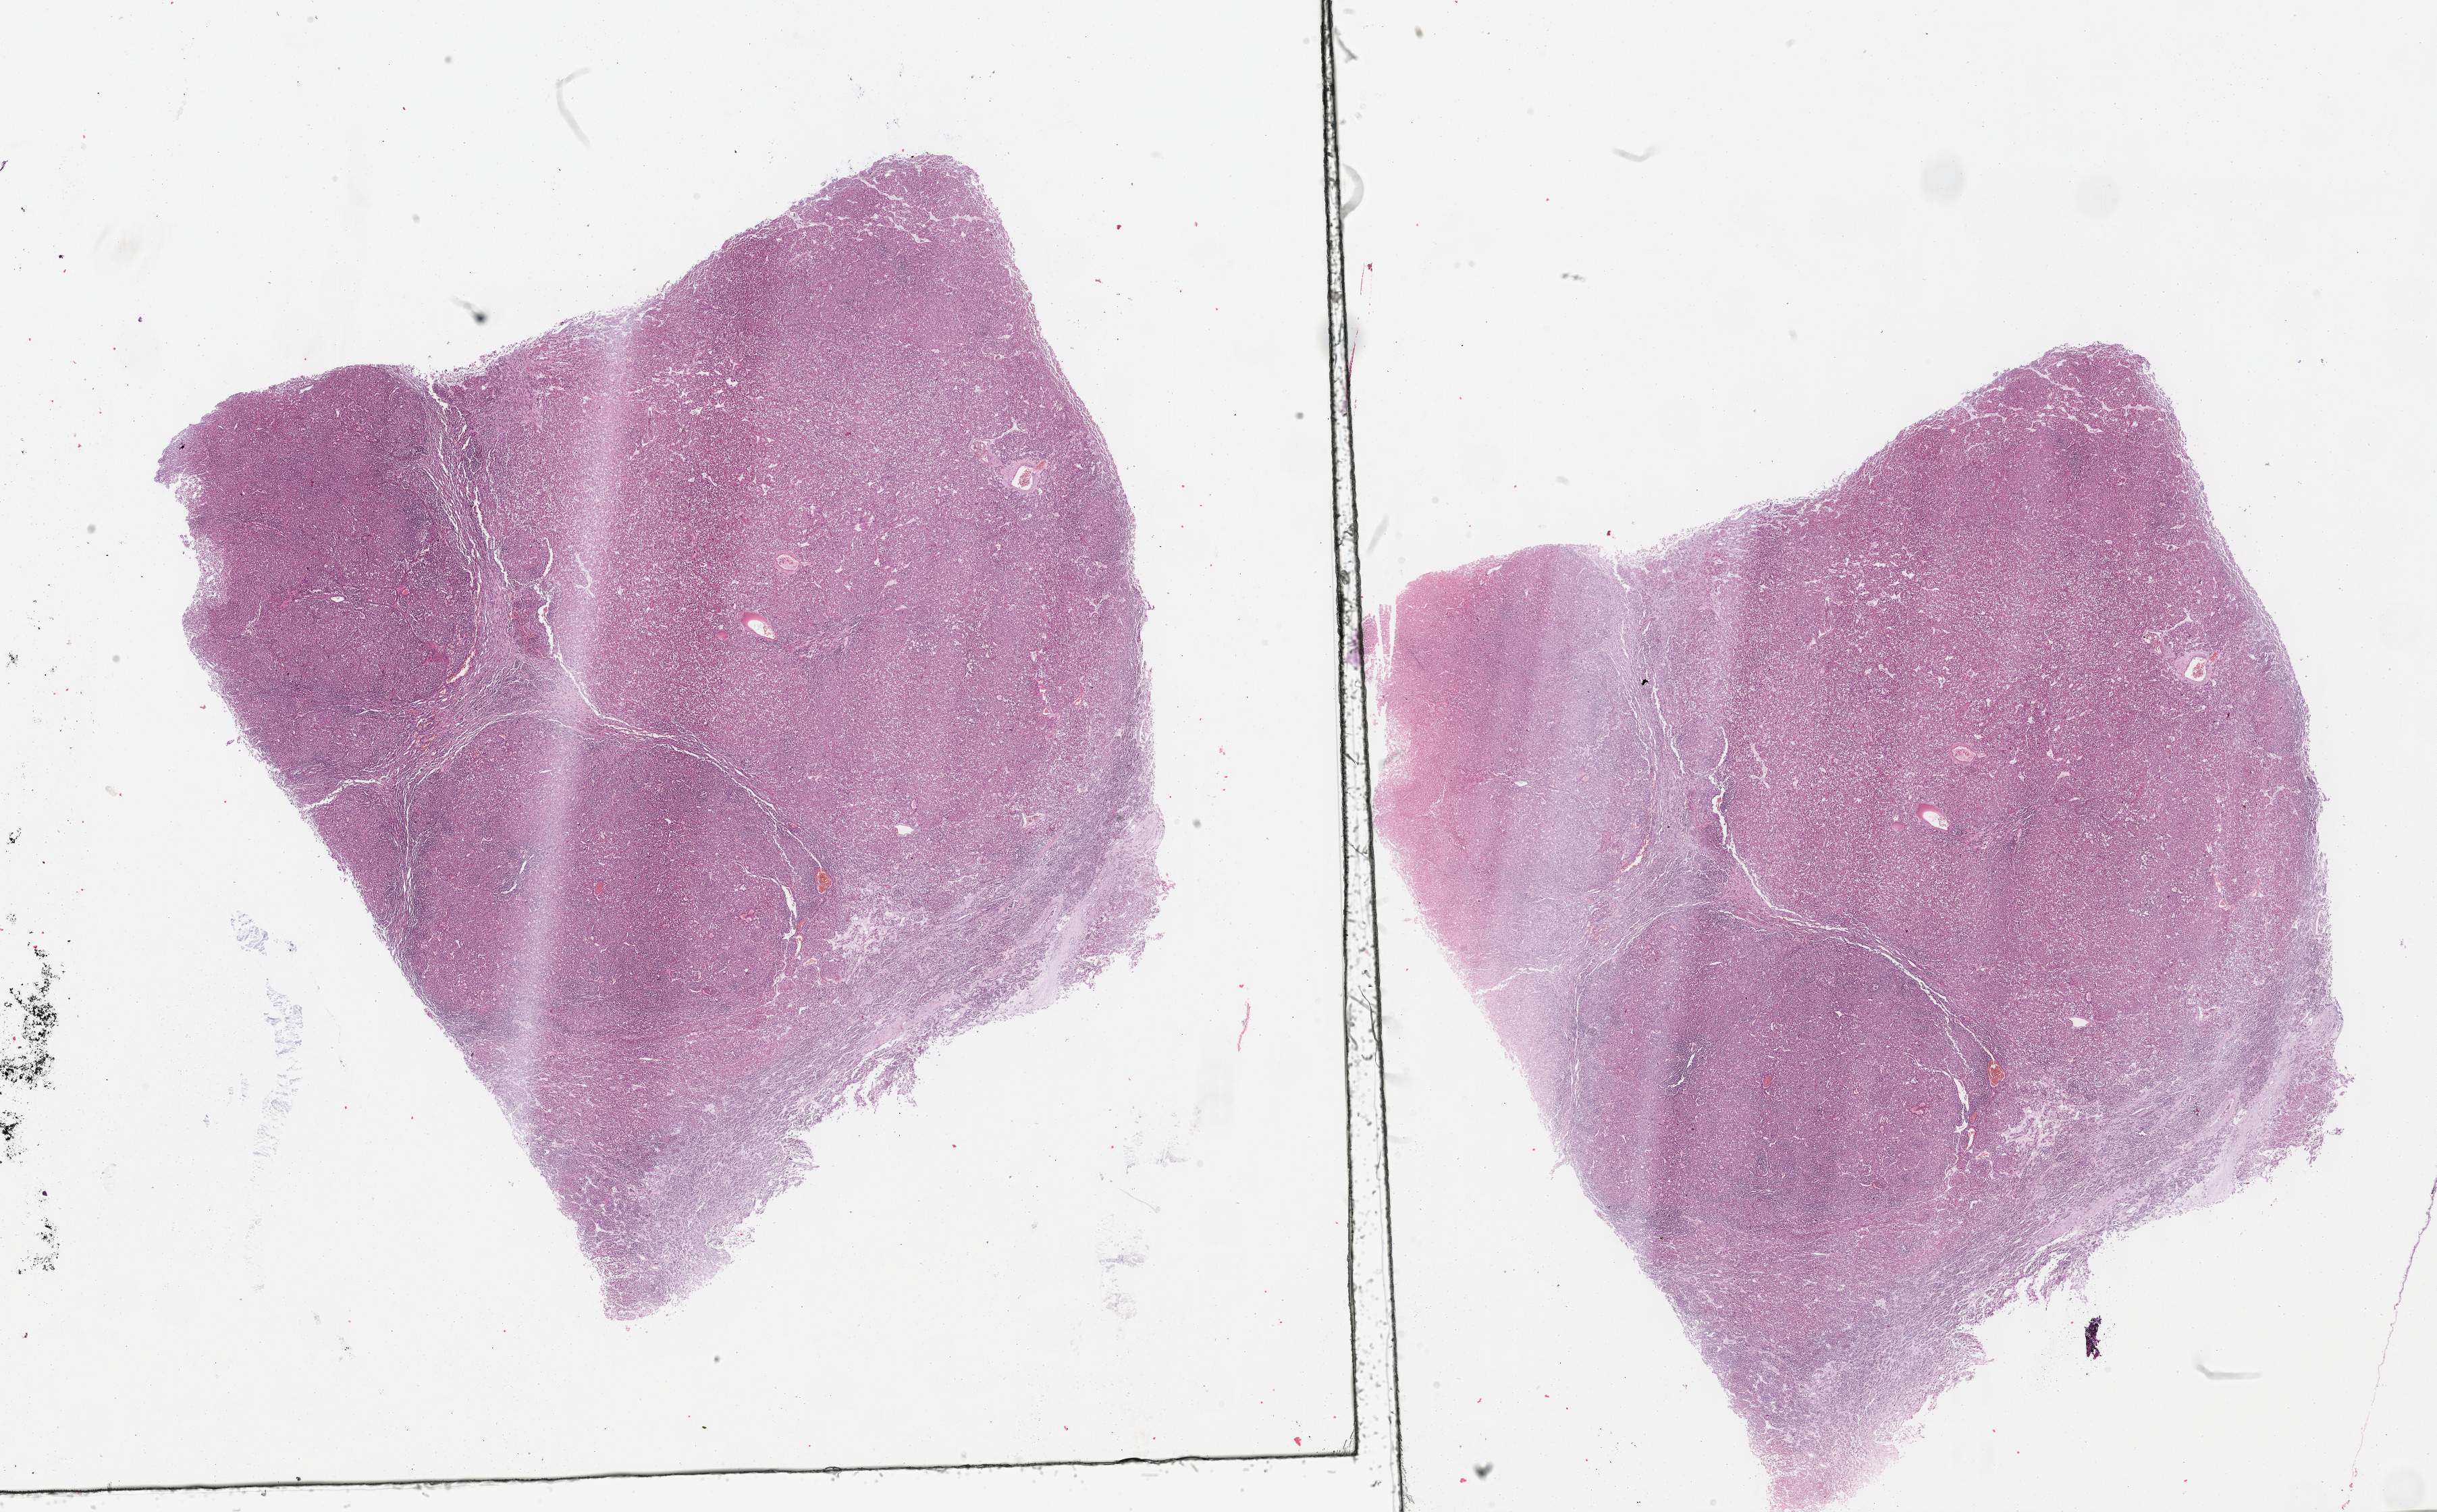
H&E-stained whole-slide image, low-resolution overview of the scanned area, about 29.2 x 18.1 mm (slide scanned at 40x), formalin-fixed paraffin-embedded (FFPE) diagnostic section, sample: primary tumour, bladder. Male, age 85 years at initial diagnosis. Histologic grade: low grade.
- histologic diagnosis: Papillary transitional cell carcinoma
- AJCC pathologic stage: II (6th edition)